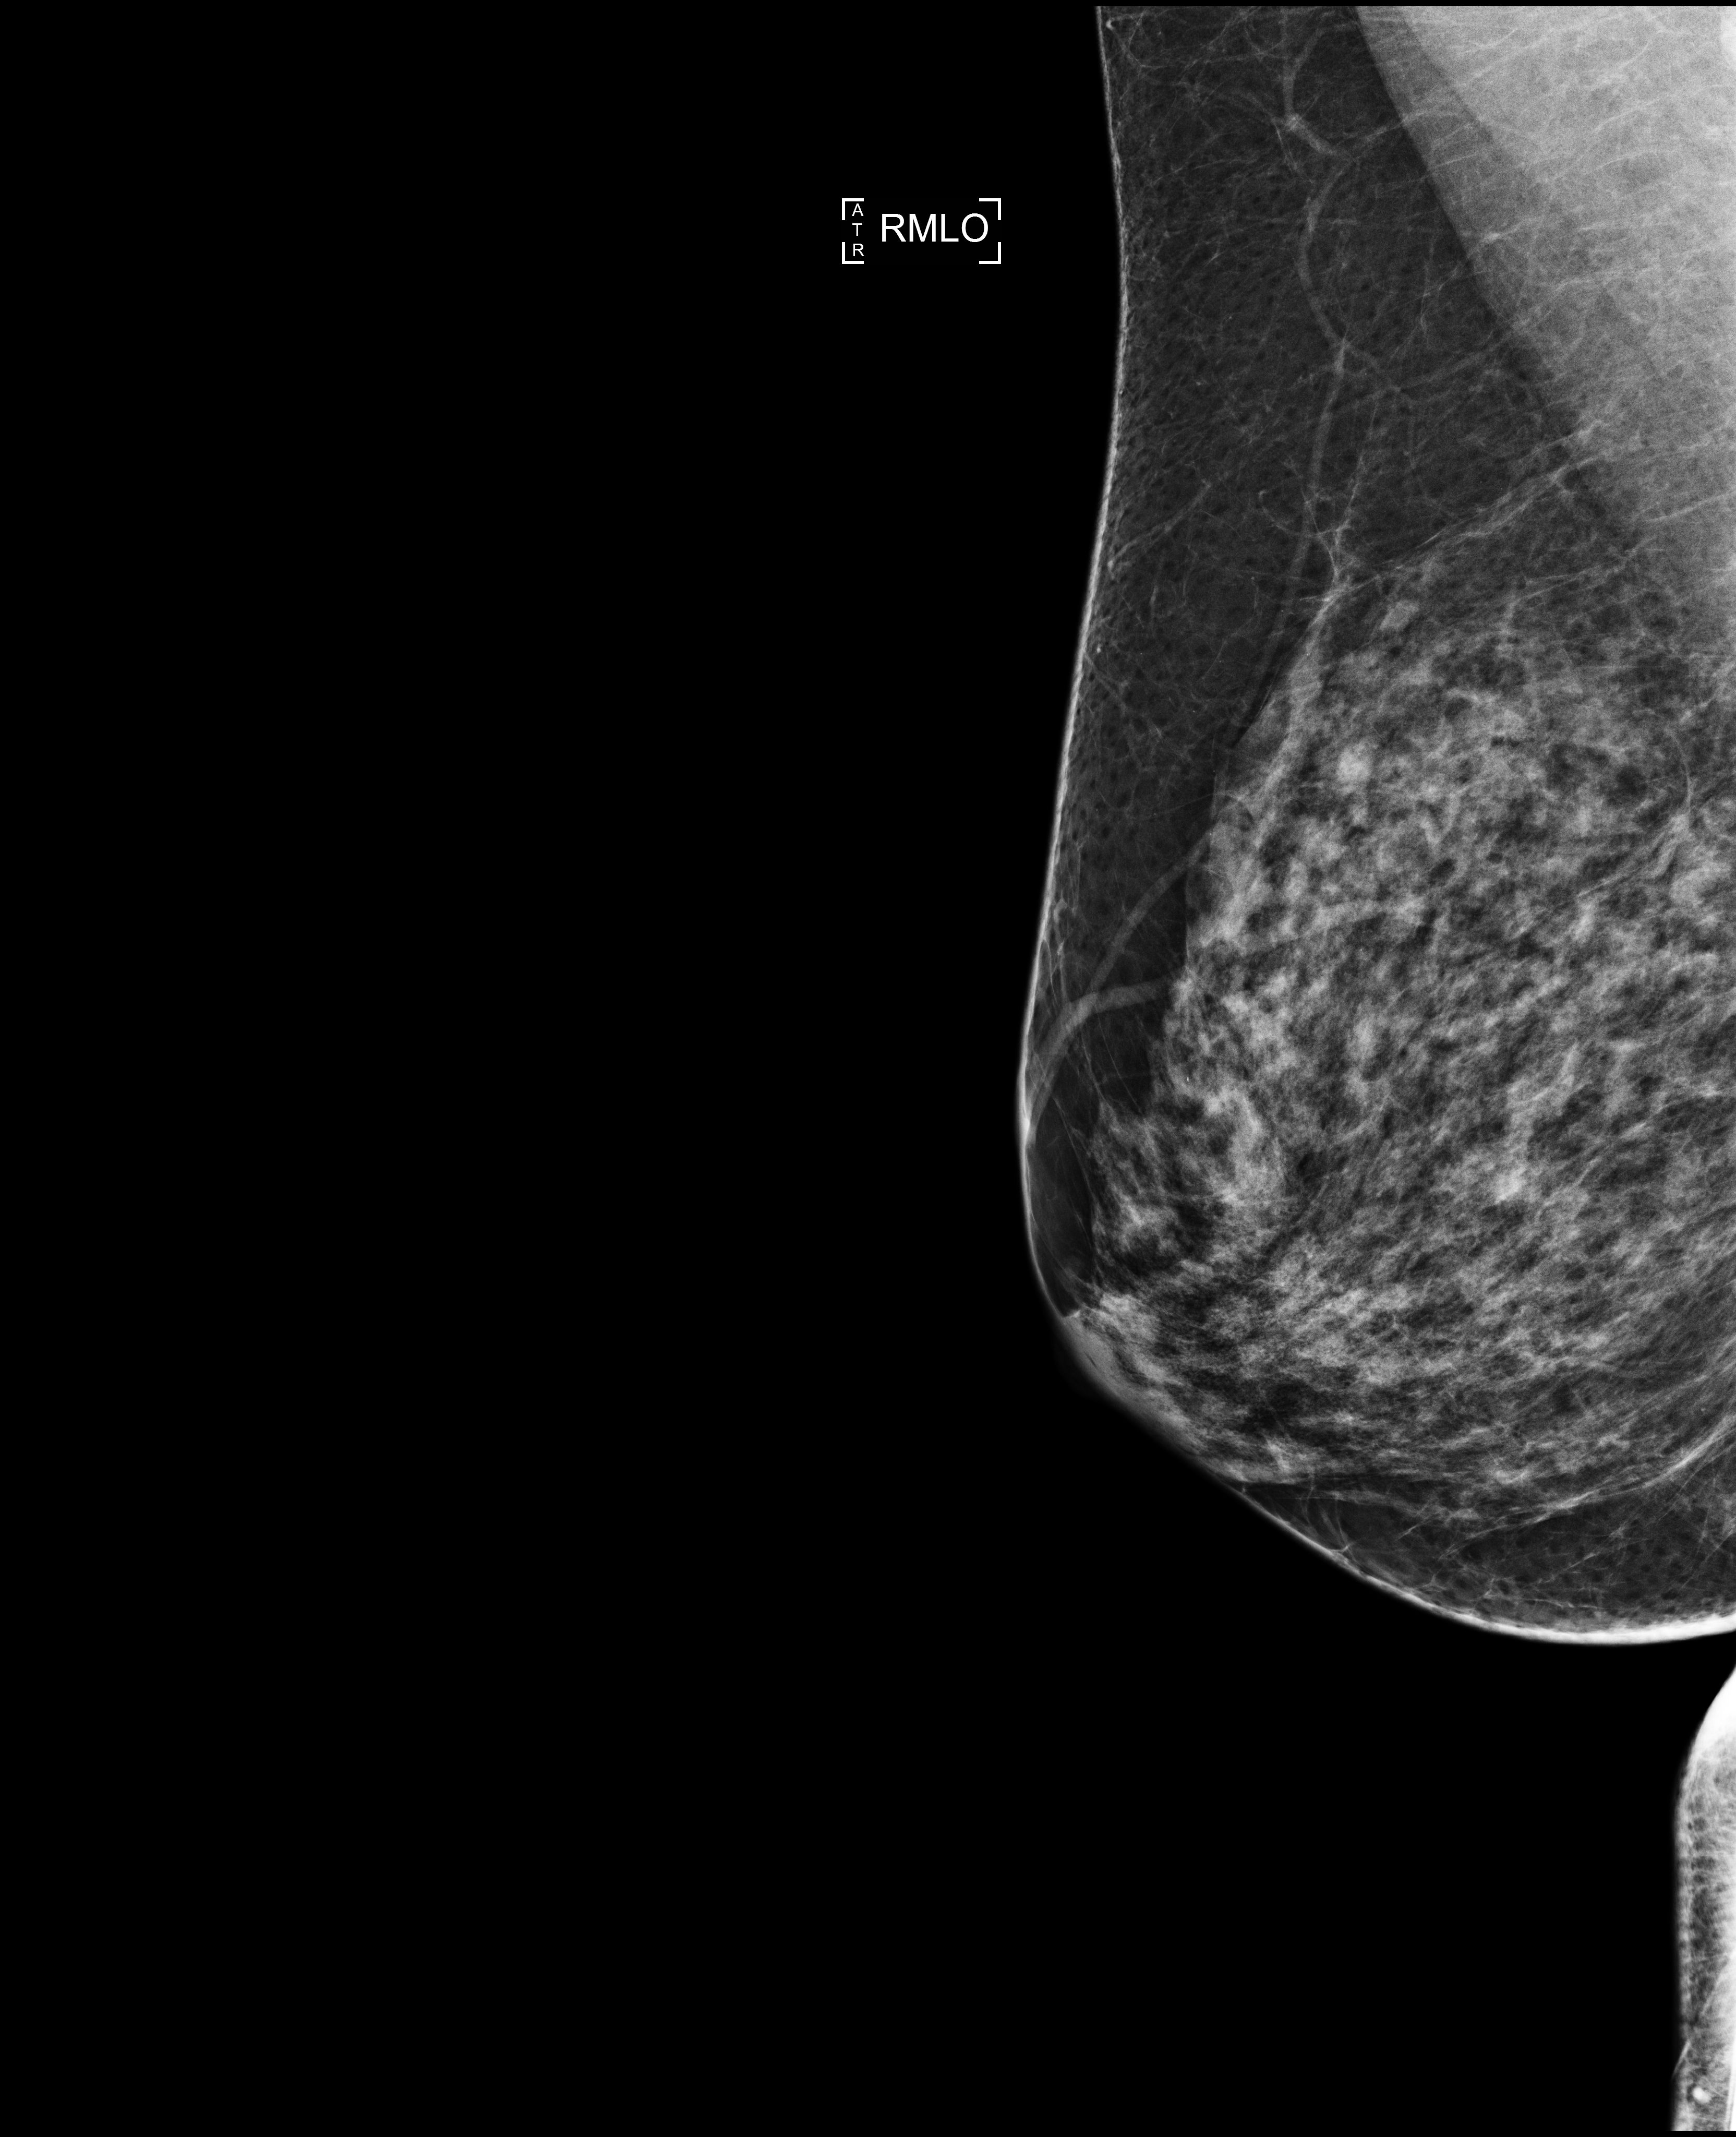
Annual screening mammography examination. Patient: female, 53 years.
Image type: full-field digital mammogram. Breast: right. Projection: MLO view.